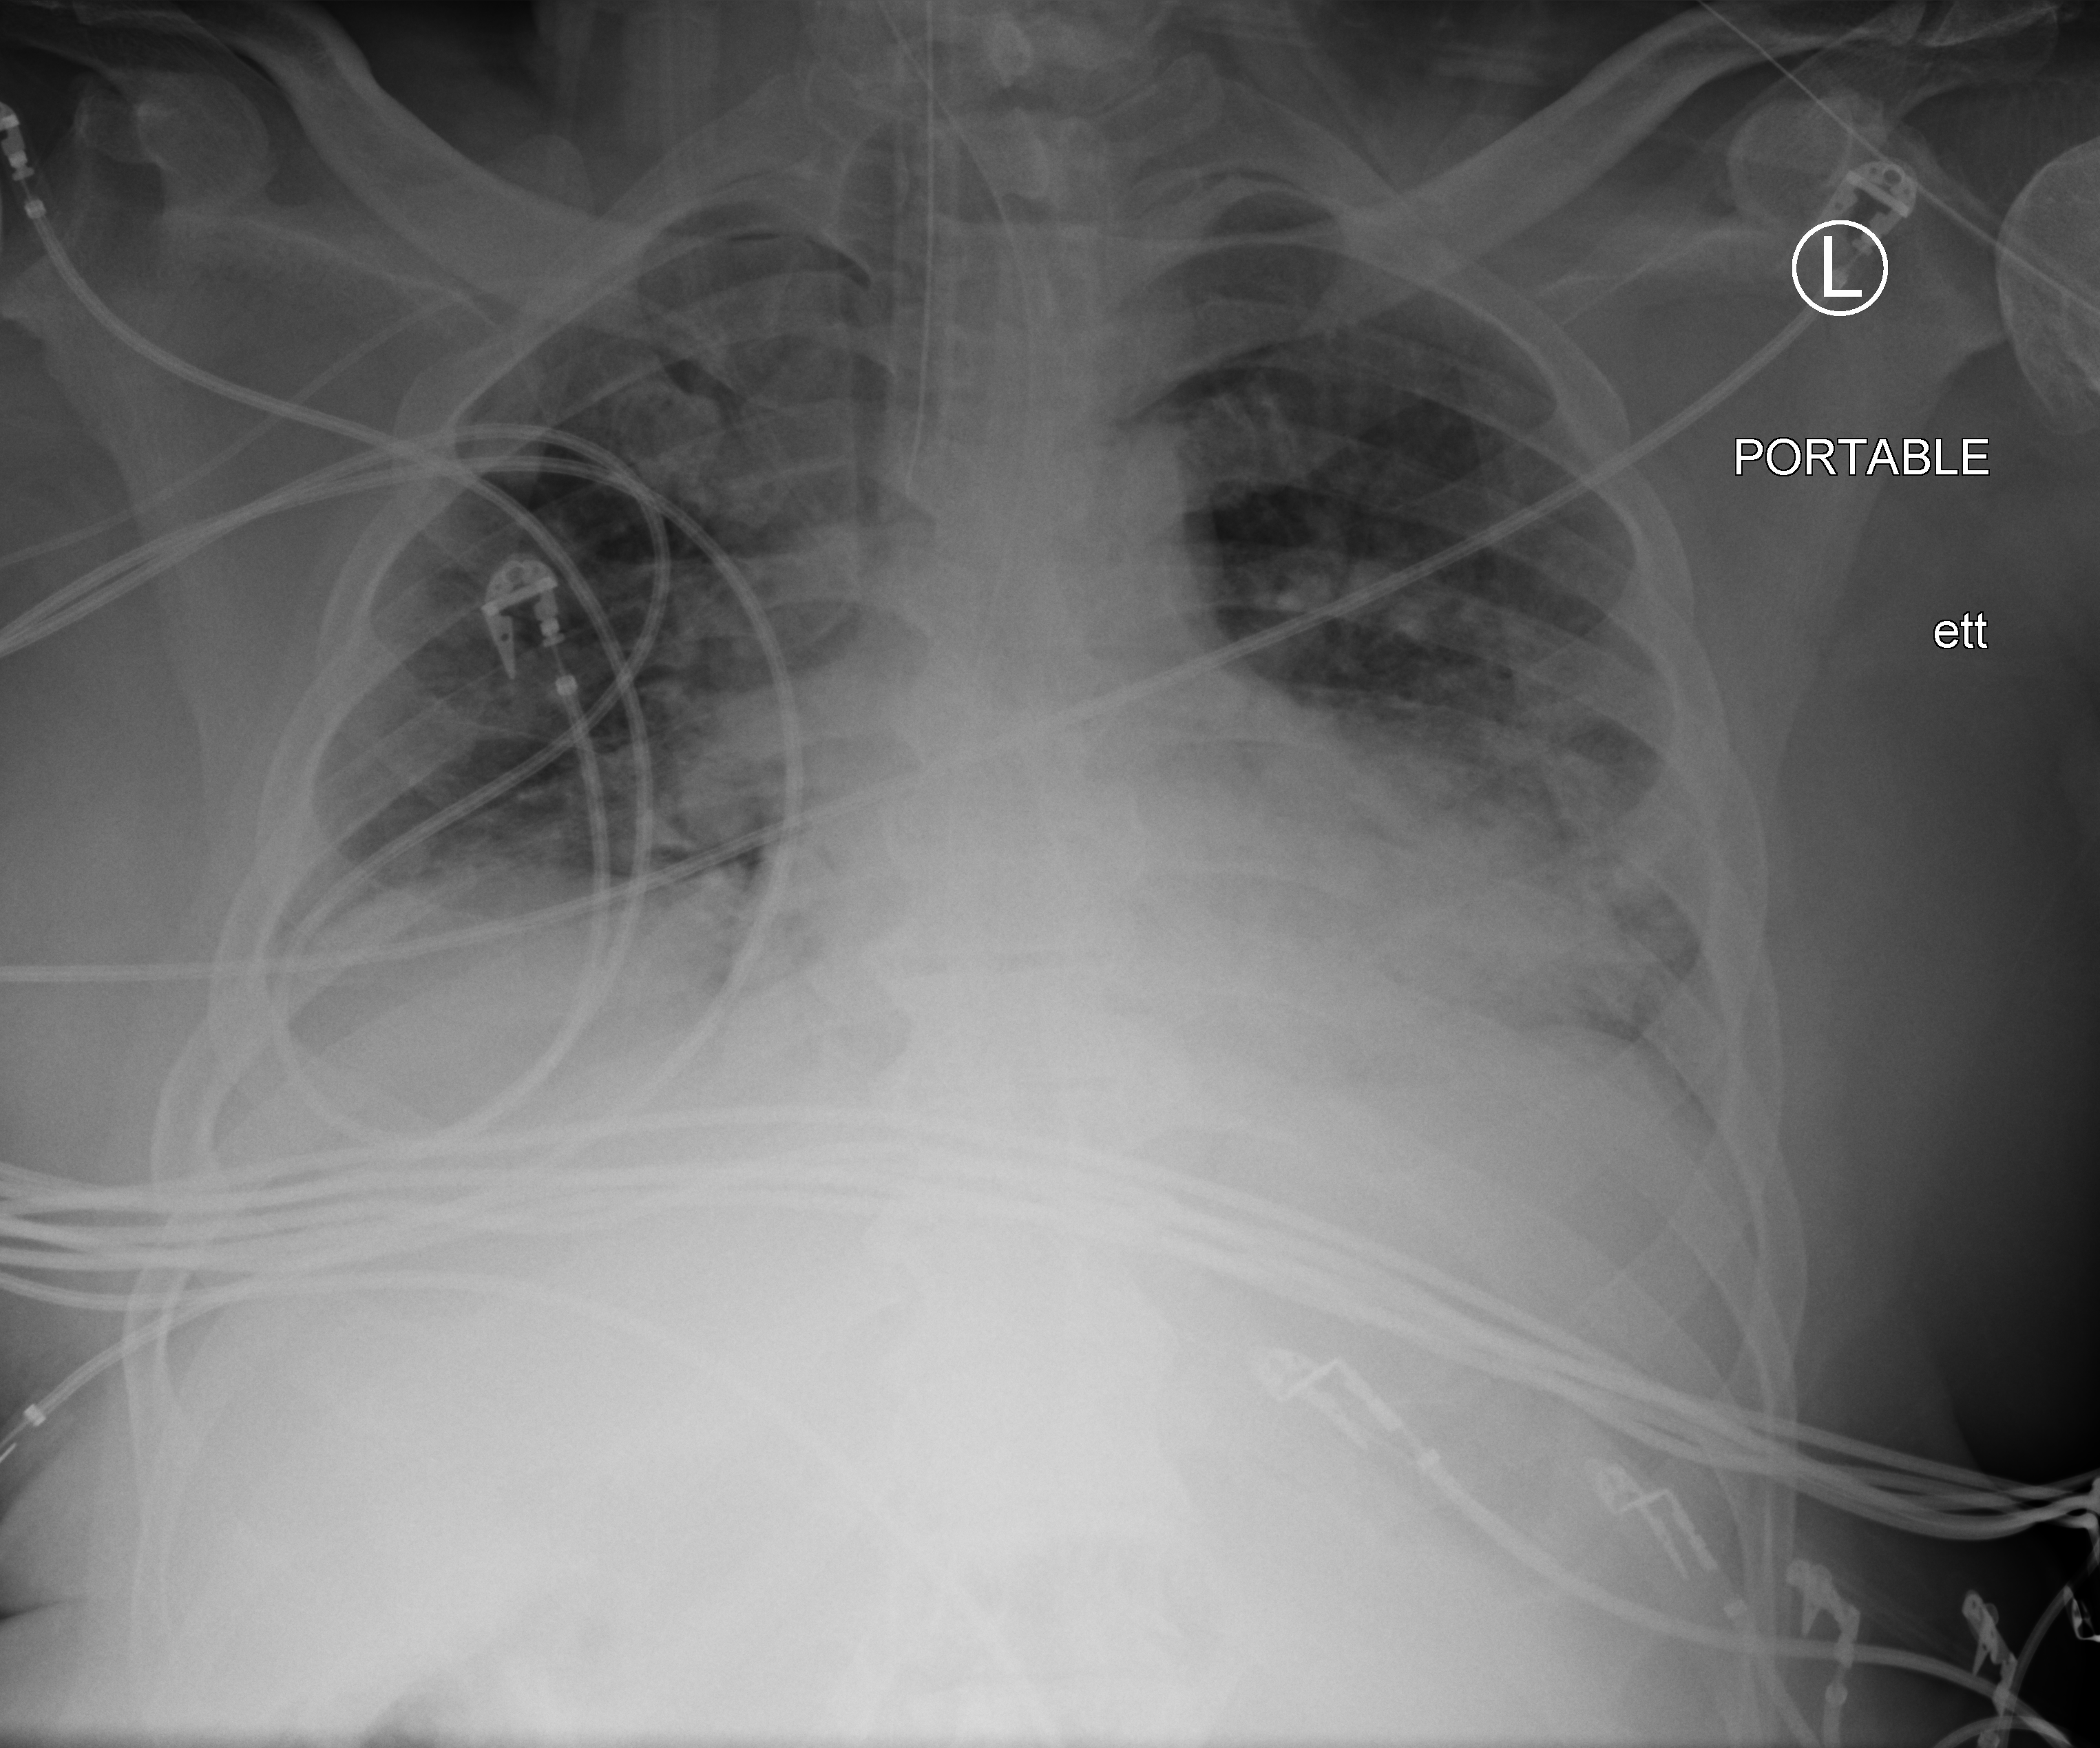
Bedside chest radiograph (computed radiography), anteroposterior (AP) projection. Male patient hospitalised with COVID-19, age 18–59 years.
From the hospital-stay record, not from the radiograph (when in the stay this image was taken is not recorded):
- smoking status (admission record): never
- admitted to intensive care during this hospital stay: yes
- mechanically ventilated during this hospital stay: yes